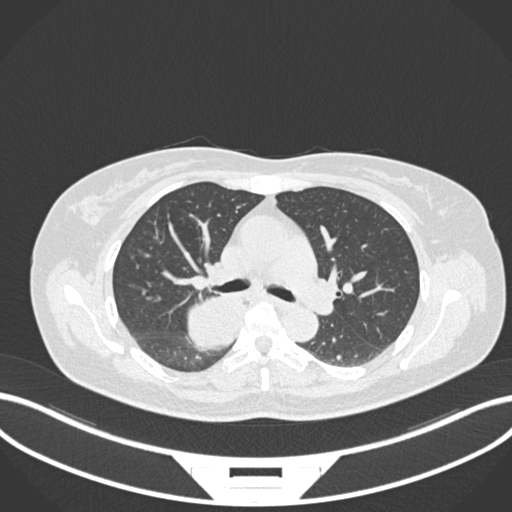
Chest CT, one axial slice; slice 616 of 677 in the series (ordered by position); 120 kVp; lung window (W 1500 / L -600 HU); 1 mm slice thickness; 512 × 512 image matrix, field of view 400 × 400 mm. Female patient, age 54 years. Case-level facts recorded for this patient, not image findings: clinical TNM (as recorded): T4 N0 M0.
Structures marked on this image (bounding box drawn by a radiologist):
- lung tumour (recorded histology: adenocarcinoma): bounding box <180,285,250,351> (left, top, right, bottom; pixels)